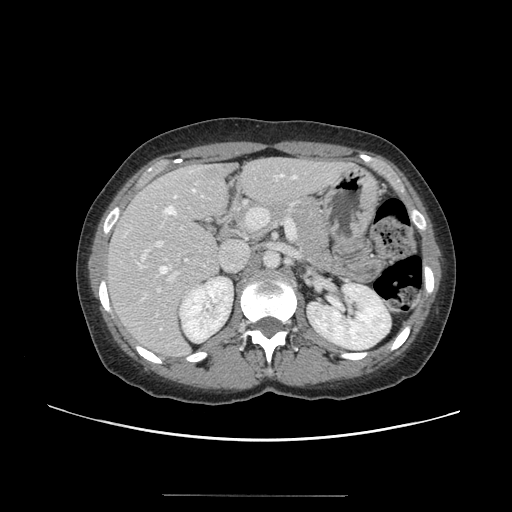
Contrast-enhanced abdominal CT, one axial slice. Position 78 of 144 along the scan axis. 120 kVp. Intravenous contrast given. Soft-tissue window (W 400 / L 40 HU). 2.5 mm slice thickness. 512 × 512 image matrix, field of view 380 × 380 mm. Female patient, age 53 years. From the clinical record (not read from this slice): diagnosis: colorectal cancer liver metastases, imaged before liver resection; multiple liver metastases: yes; largest metastasis: 1.1 cm.
Structures marked on this image (expert manual segmentation):
- hepatic veins: bounding box (x1, y1, x2, y2) in pixels: (160, 174, 296, 329)
- liver: (108, 159, 345, 357)
- planned liver remnant (the part of the liver to remain after resection): (108, 159, 318, 299)
- portal vein (with intrahepatic branches): (137, 202, 296, 292)